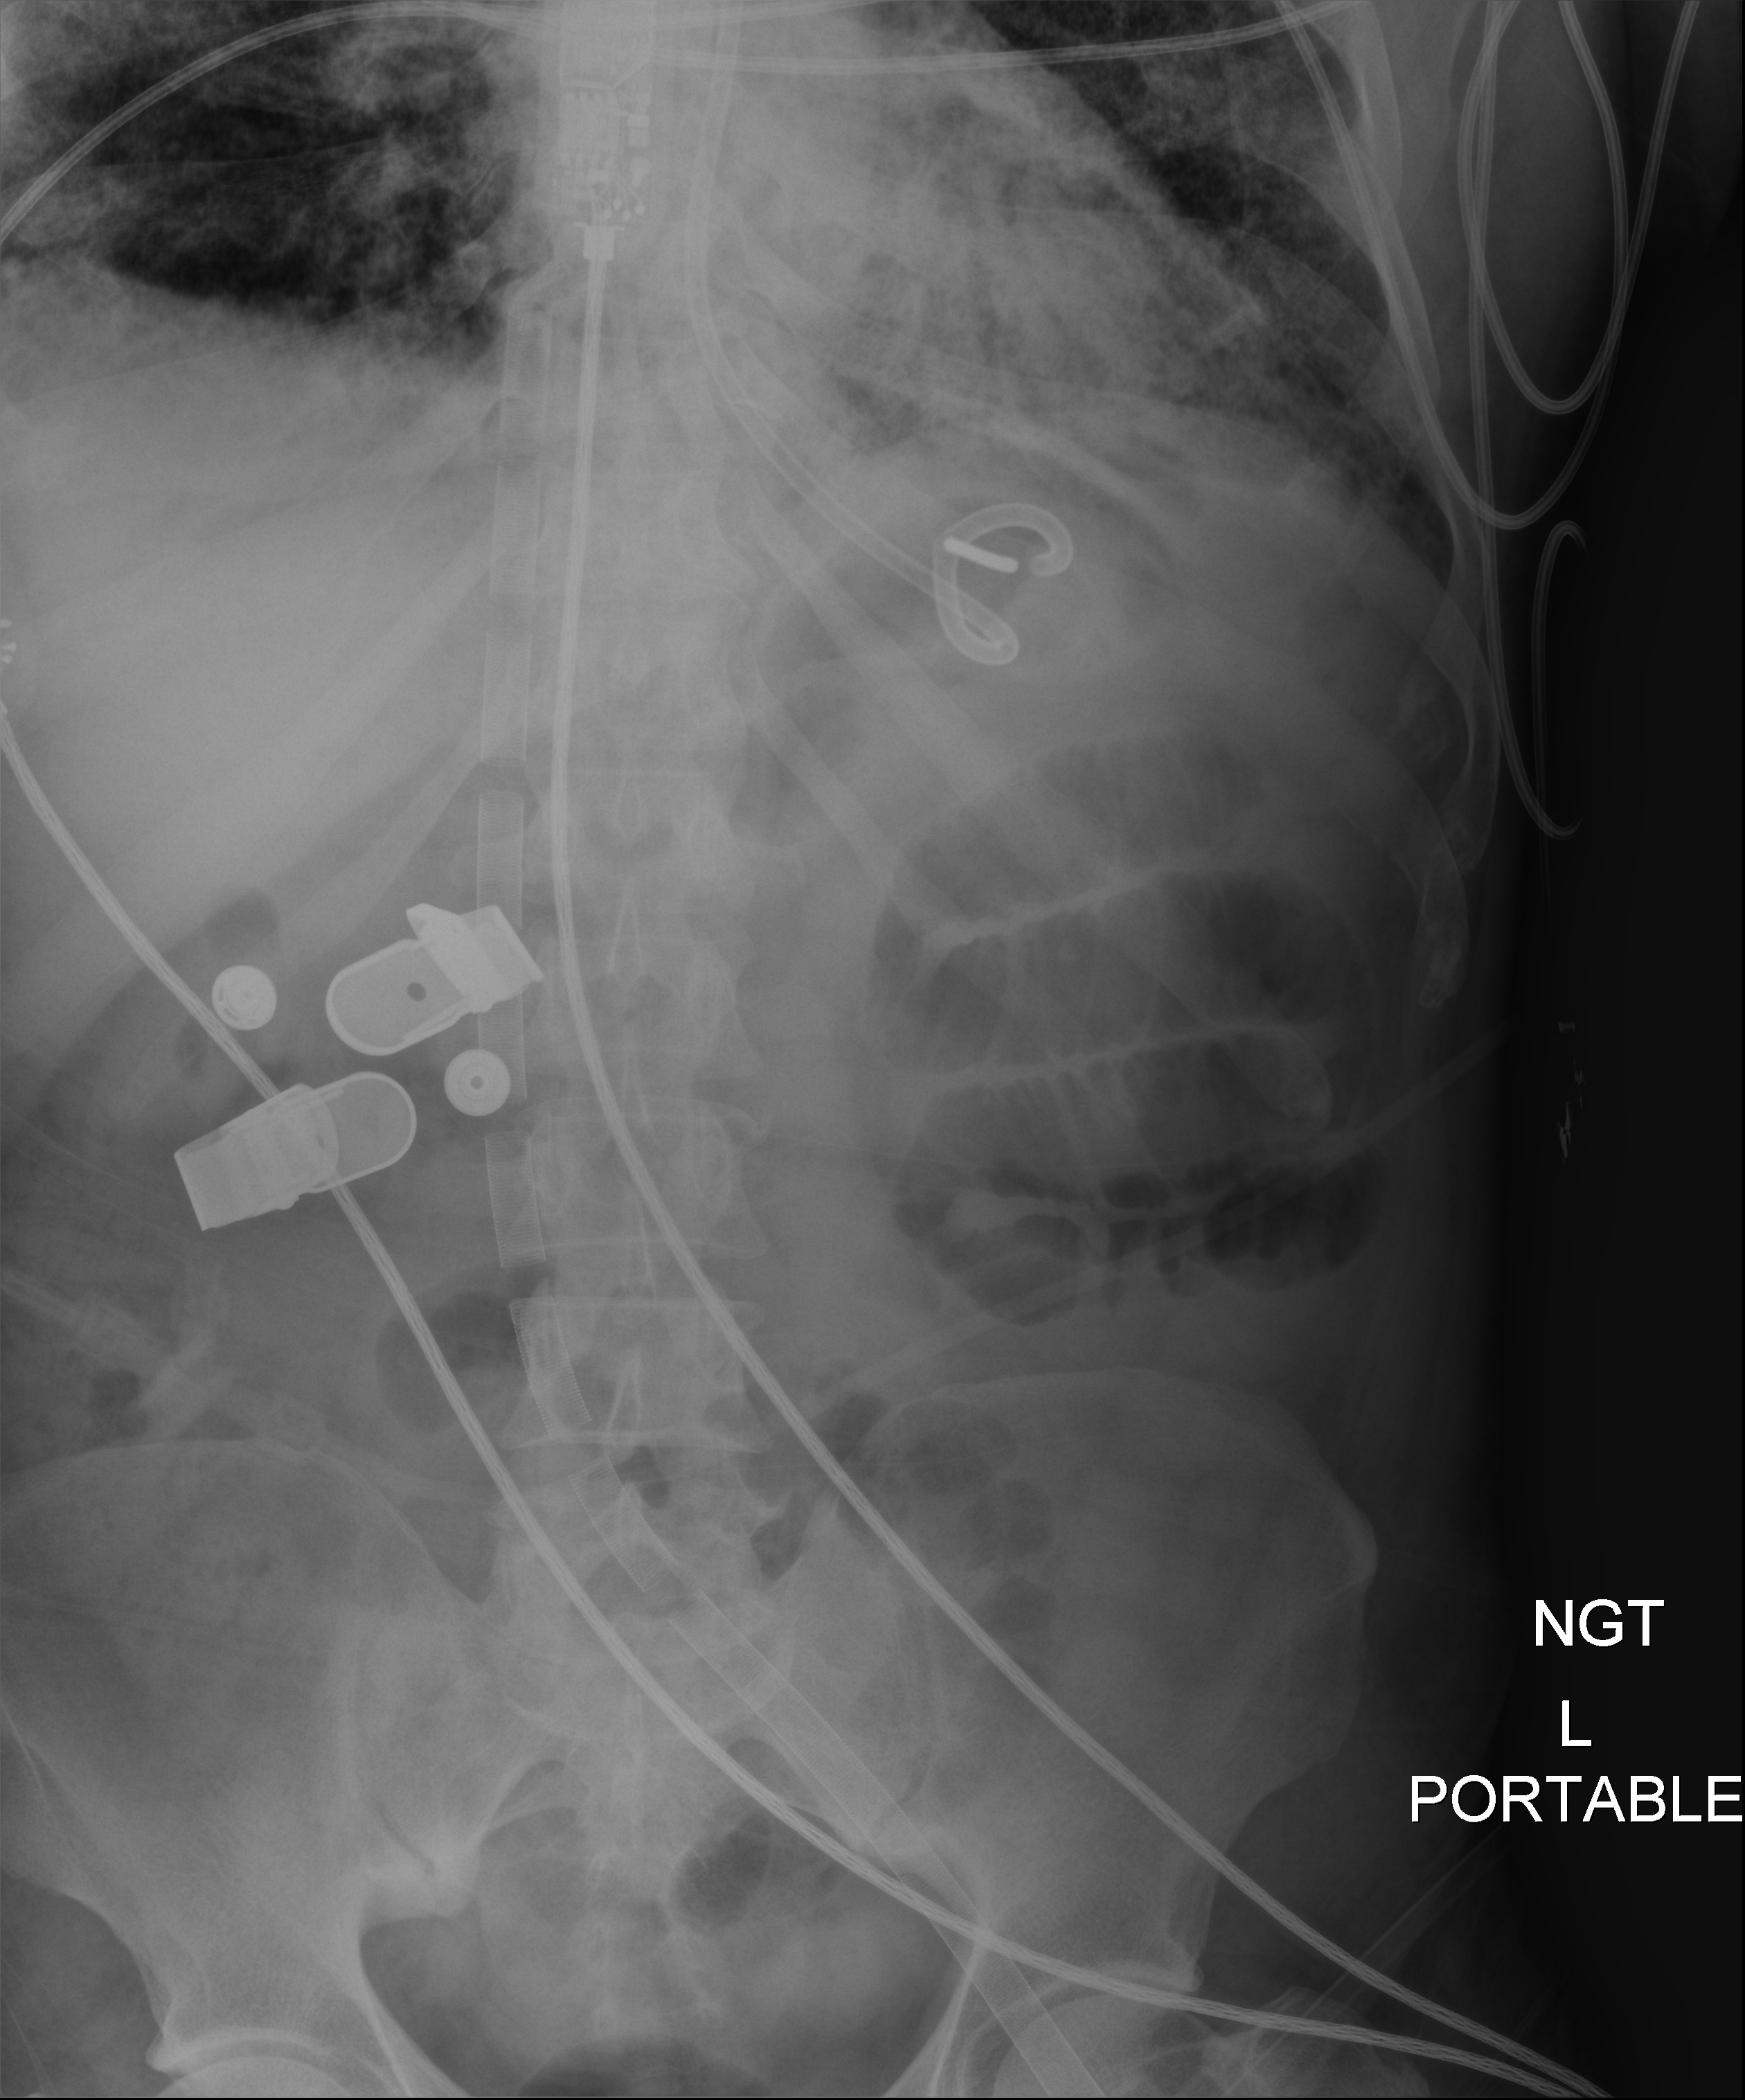
Abdomen radiograph; anteroposterior (AP) projection. Patient hospitalised with COVID-19; male, aged 18–59 years.
From the hospital-stay record, not from the radiograph (when in the stay this image was taken is not recorded): smoking status (admission record): never.